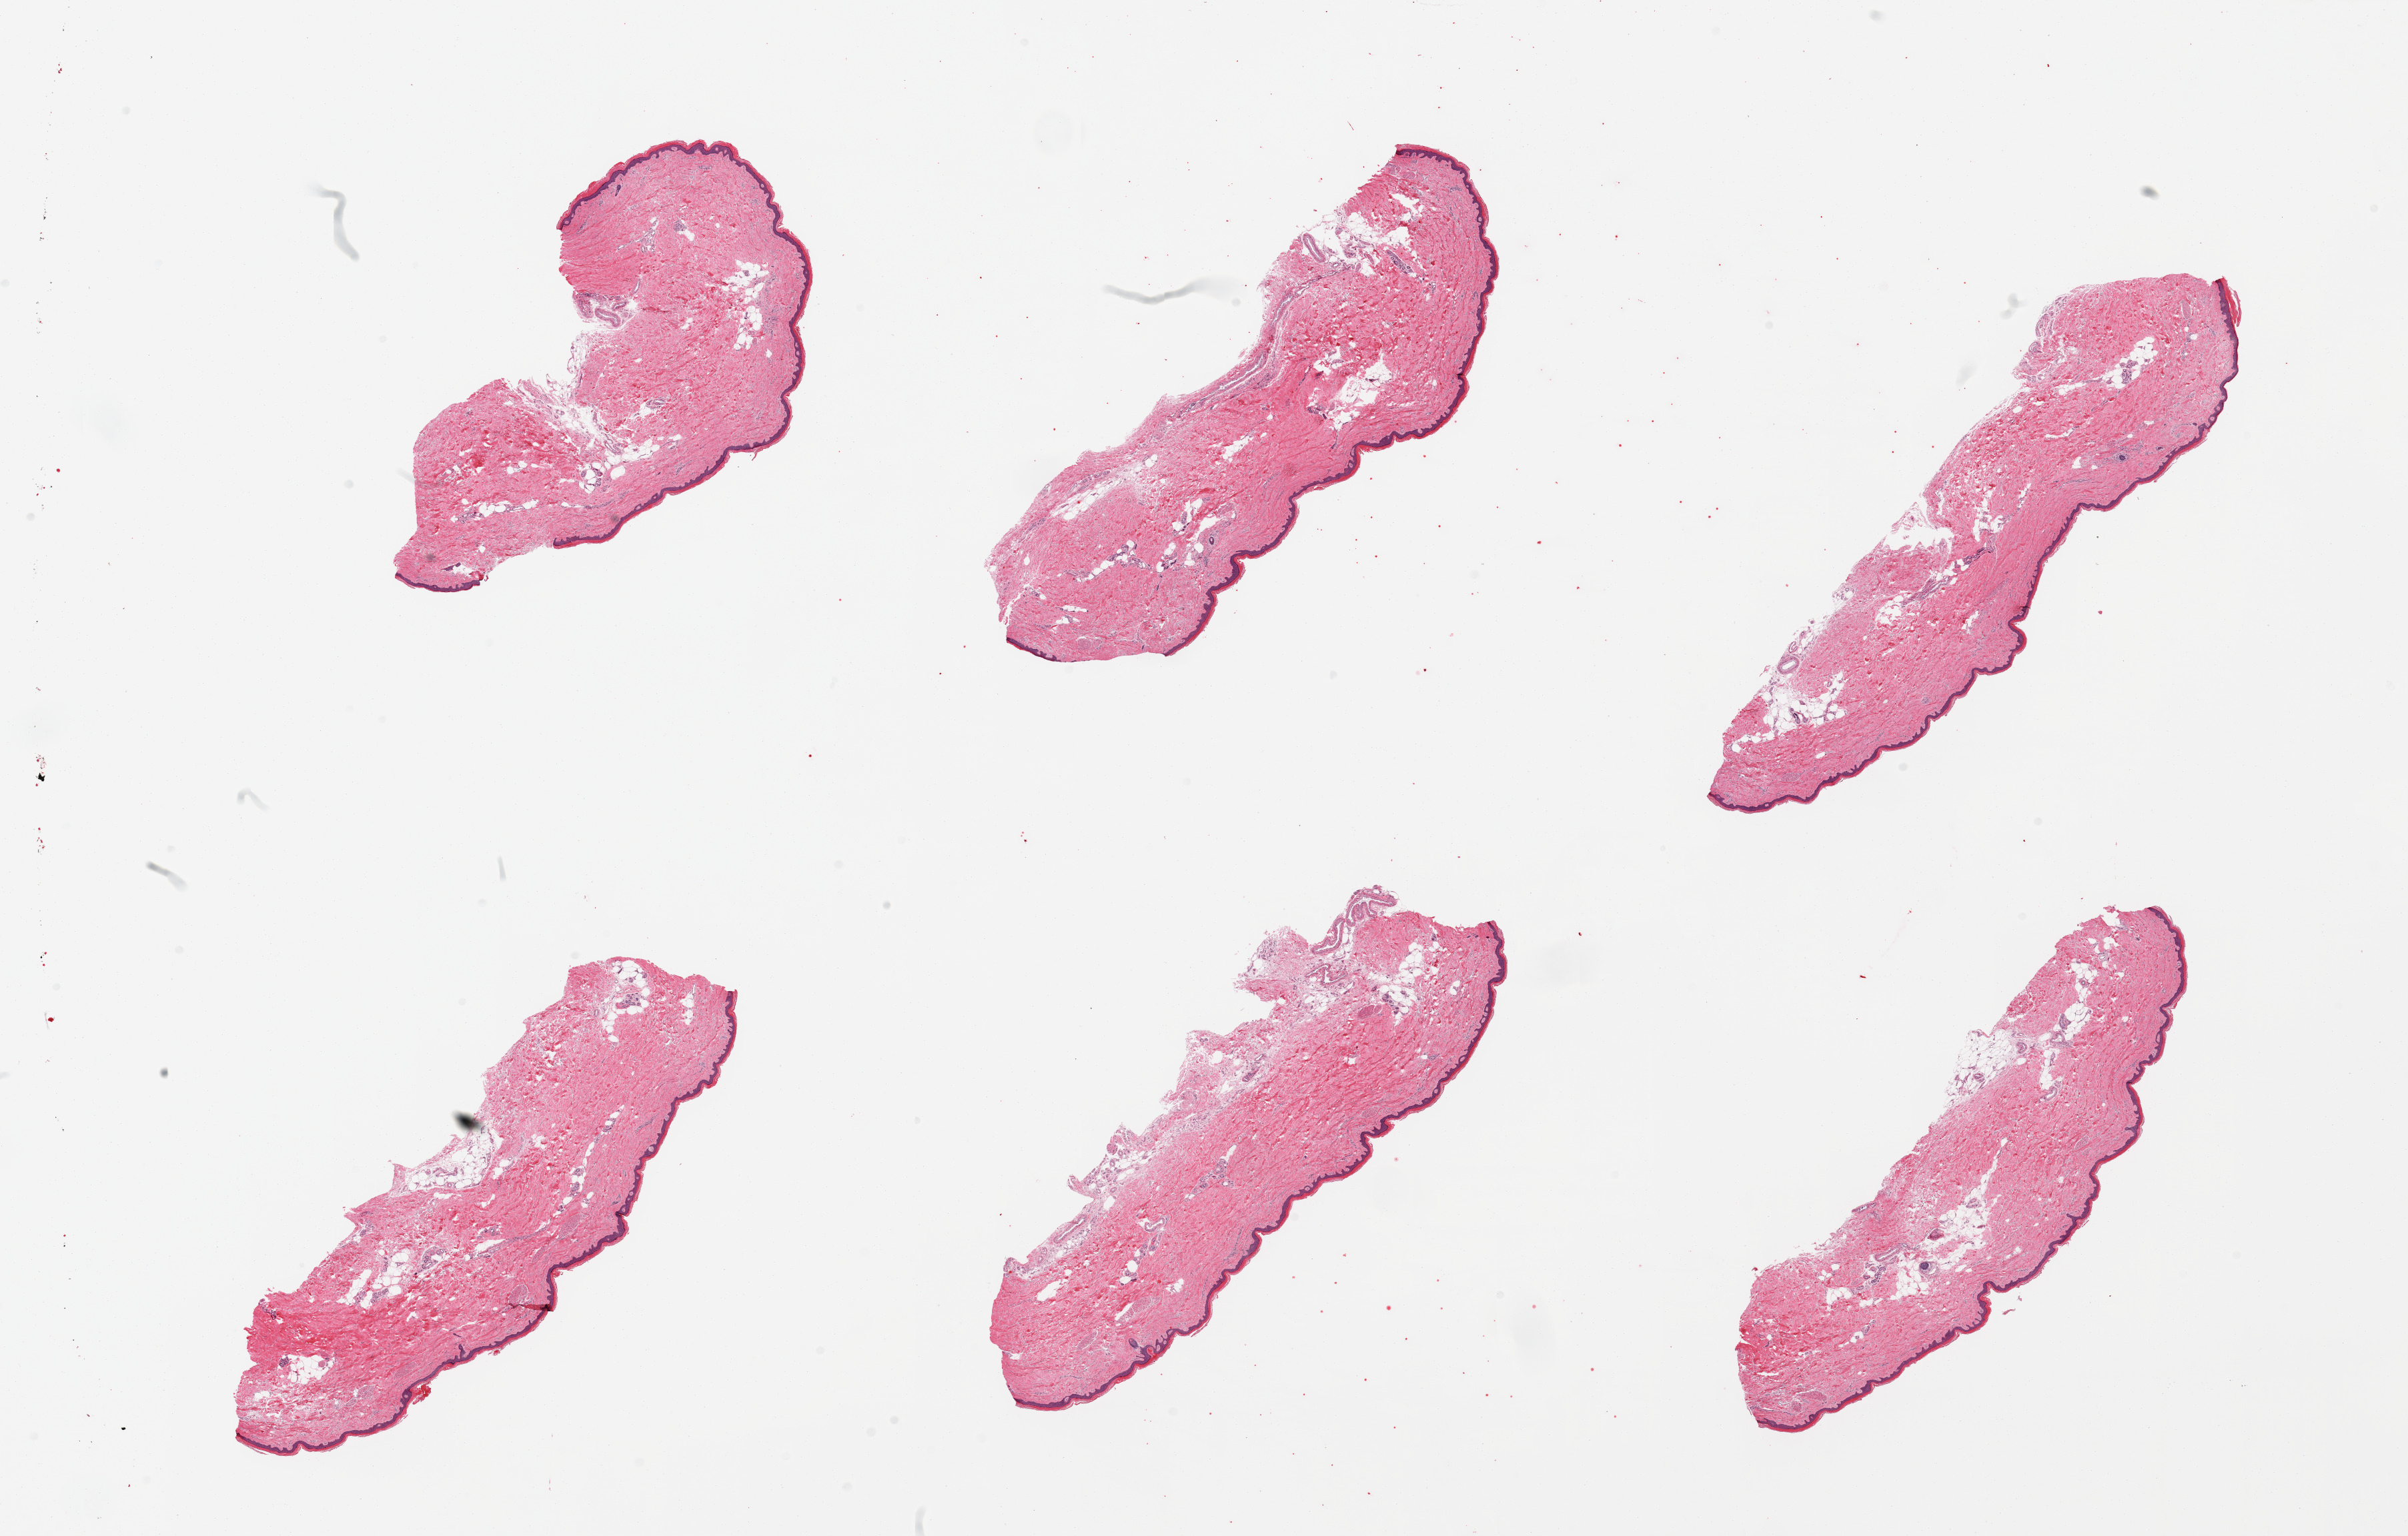
H&E whole-slide image, brightfield, a low-resolution overview of the entire scanned area, about 28.5 x 18.2 mm (slide scanned at 20x); PAXgene-fixed paraffin-embedded (PFPE) section; target tissue: skin of lower leg; tissue donor sample. Donor: female.
Review note (as recorded): 6 pieces; 10 to 20% mostly internal (periadnexal) fat; epidermis measures ~39 microns.